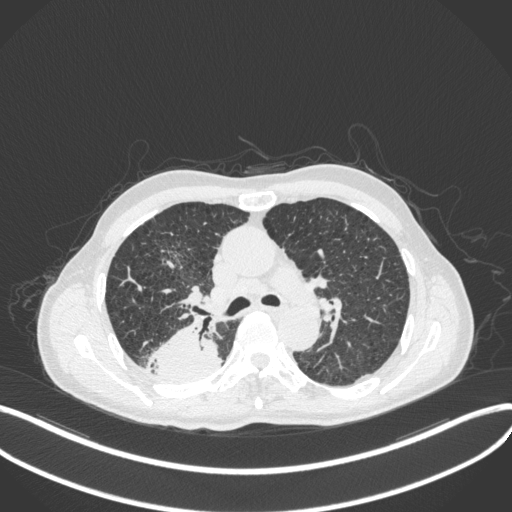
Chest CT, one axial slice; position 293 of 423 along the scan axis; reconstruction kernel B31f; lung window (W 1500 / L -600 HU); 512 × 512 image matrix, field of view 400 × 400 mm. Male patient, age 79 years. Case-level facts recorded for this patient, not image findings: clinical TNM (as recorded): T3 N0 M0.
Structures marked on this image (bounding box drawn by a radiologist):
- lung tumour (recorded histology: adenocarcinoma): box from (x=146, y=317) to (x=223, y=382) px